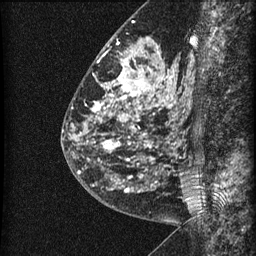
Breast MRI (dynamic contrast-enhanced), one sagittal slice. Position 24 of 60 along the scan axis. Dynamic contrast-enhanced series, image 2 of 3 at this slice position (ordered by acquisition). 1.5 T. TE 4.2 ms, TR 22.7 ms. 1.5 mm slice thickness. 256 × 256 image matrix, field of view 180 × 180 mm. Female patient, age 48 years. Case-level facts recorded for this patient, not image findings: setting: breast cancer imaged before/during neoadjuvant chemotherapy; receptor status: triple-negative.
Structures marked on this image (semi-automatically segmented with operator editing):
- analysis volume of interest (the breast-tissue region the enhancement analysis was run in; not a lesion): bounding box <81,23,186,202> (left, top, right, bottom; pixels)
- tumour enhancement mask (voxels above the 90 % enhancement threshold inside the analysis volume of interest): <87,39,175,192>